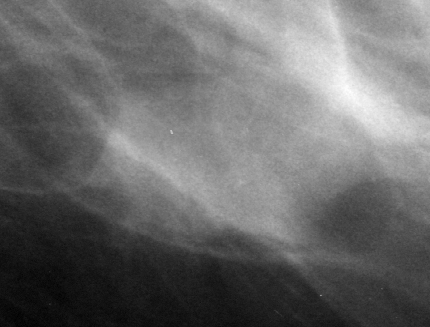
Cropped region of a digitized screen-film mammogram centred on a radiologist-marked abnormality, left breast, MLO view, BI-RADS breast density category 2 (scale 1–4).
Marked abnormality: mass, shape irregular, margins ill defined; BI-RADS assessment category 4; subtlety rating 3 on a 1 (subtle) to 5 (obvious) scale; pathology (as recorded): malignant.